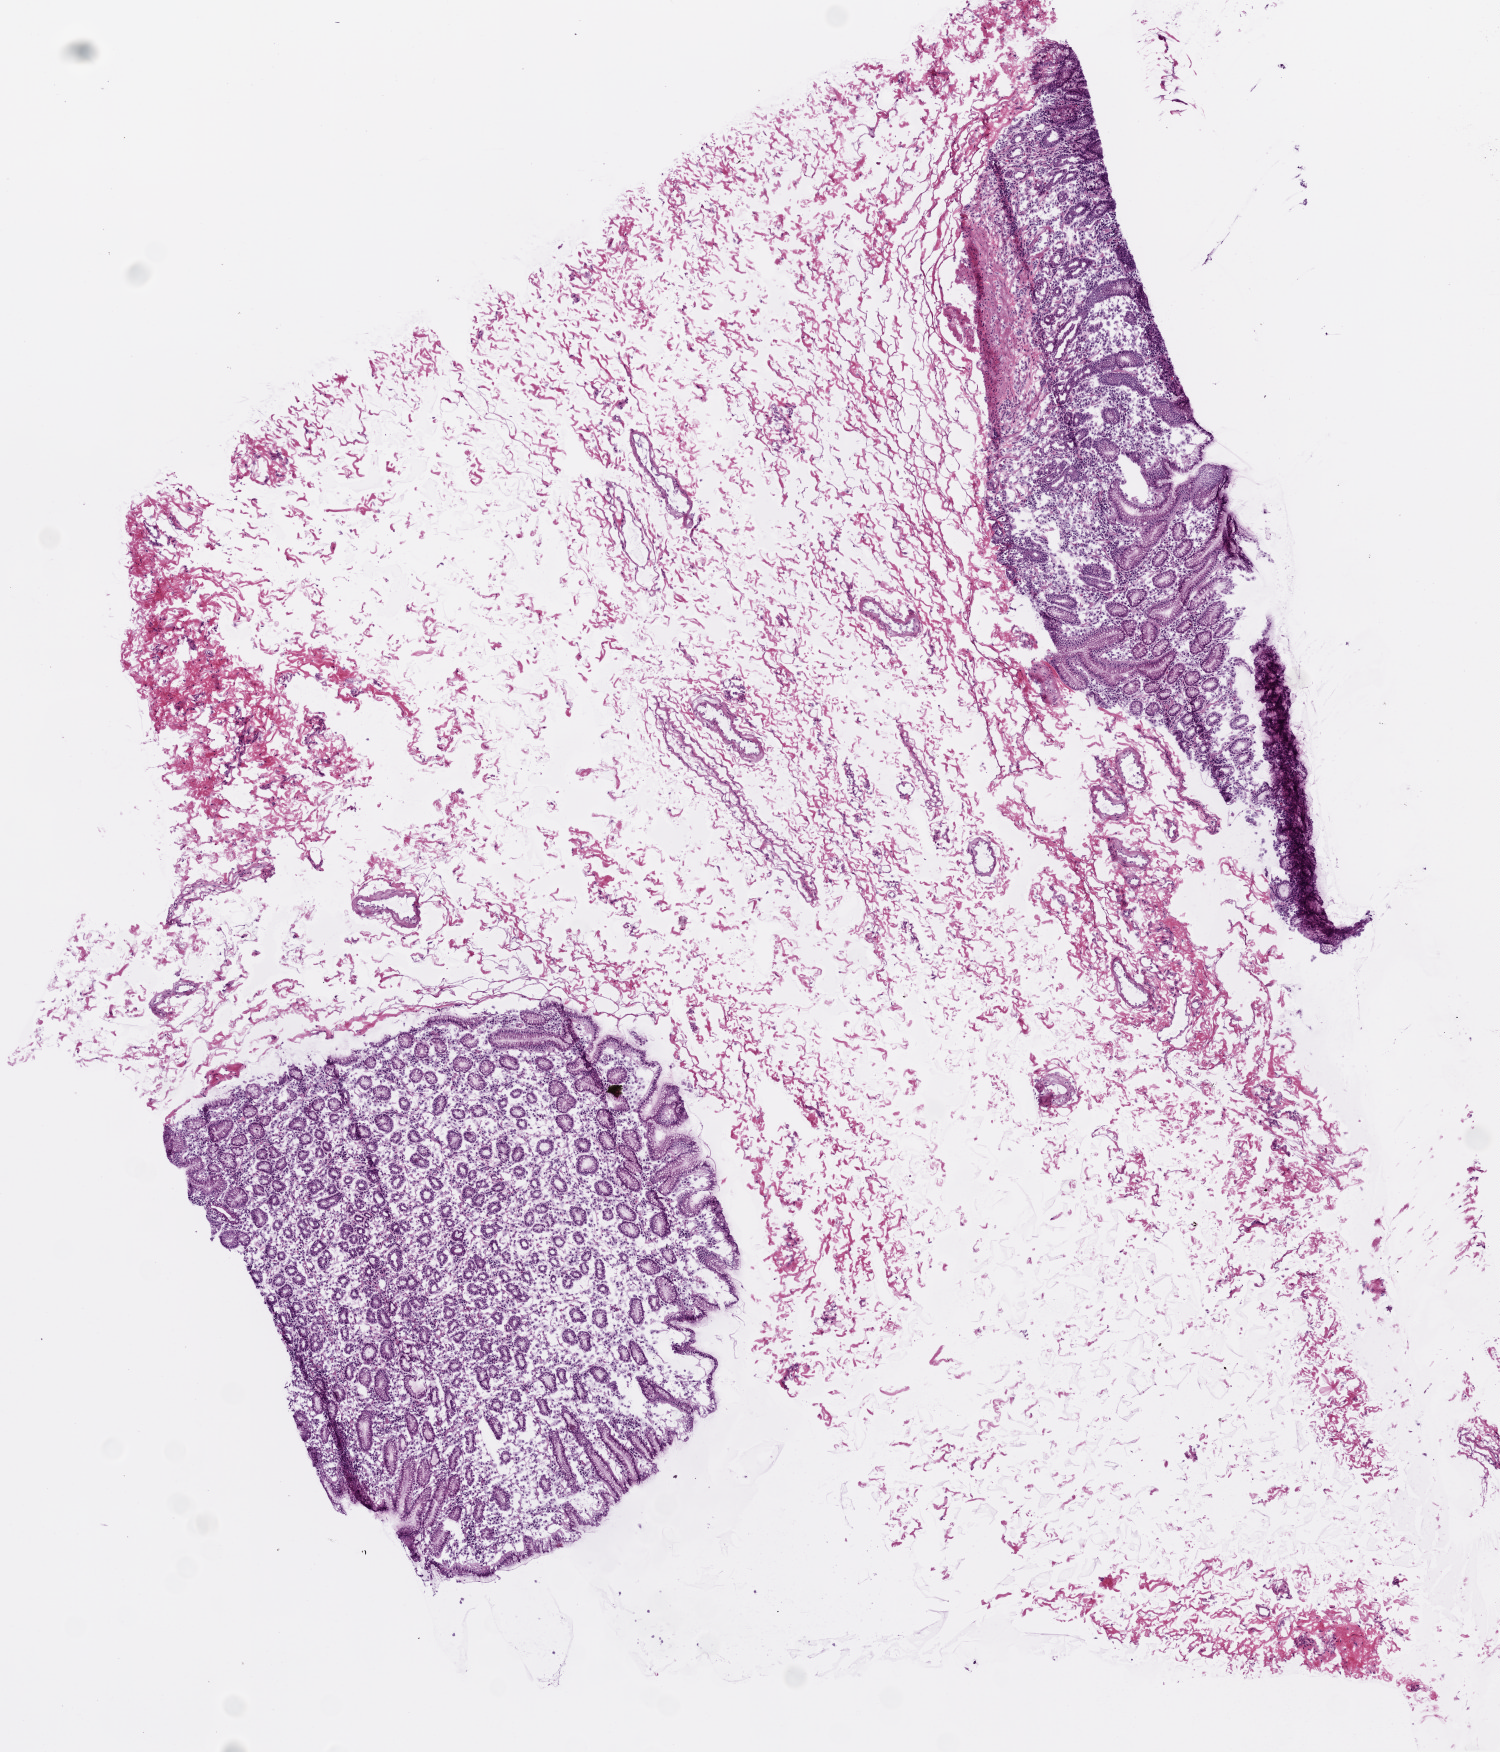
Whole-slide histology image, Hematoxylin and eosin (H&E) stained, shown as a low-resolution overview of the whole scanned area (about 6.0 x 7.0 mm, slide scanned at 20x). Frozen section from the top of the tissue portion. Sample: solid tissue normal (non-tumour tissue), stomach. Male, age 66 years at initial diagnosis.
This section: solid tissue normal sample (biorepository sample class). Patient diagnosis: Adenocarcinoma, intestinal type (body of stomach).